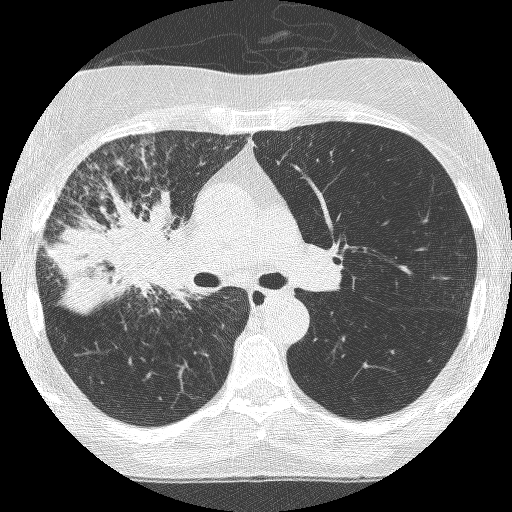
Axial slice from a low-dose chest CT screening exam. Third annual screen. Lung window (W 1500 / L -600 HU). 120 kVp. Slice 160 of 253 in the series. 512 × 512 image matrix, field of view 294 × 294 mm. Female, age 64 years at enrolment. Former smoker at enrolment.
Expert reader's lesion annotation, bounding box (x1, y1, x2, y2) in pixels: (78, 200, 204, 327). The exam's reader record, not a measurement of the box and not confirmed to be the same lesion: non-calcified nodule or mass ≥4 mm, right upper lobe, 49 × 43 mm, spiculated (stellate) margins, soft tissue attenuation, pre-existing on the prior screen: yes; interval growth: yes. Official screen result: positive, other. Participant outcome: lung cancer diagnosed 7 days after this screen — adenocarcinoma, NOS, right upper lobe, right middle lobe, right hilum, stage IV (AJCC 6th edition), 85 mm at pathology.